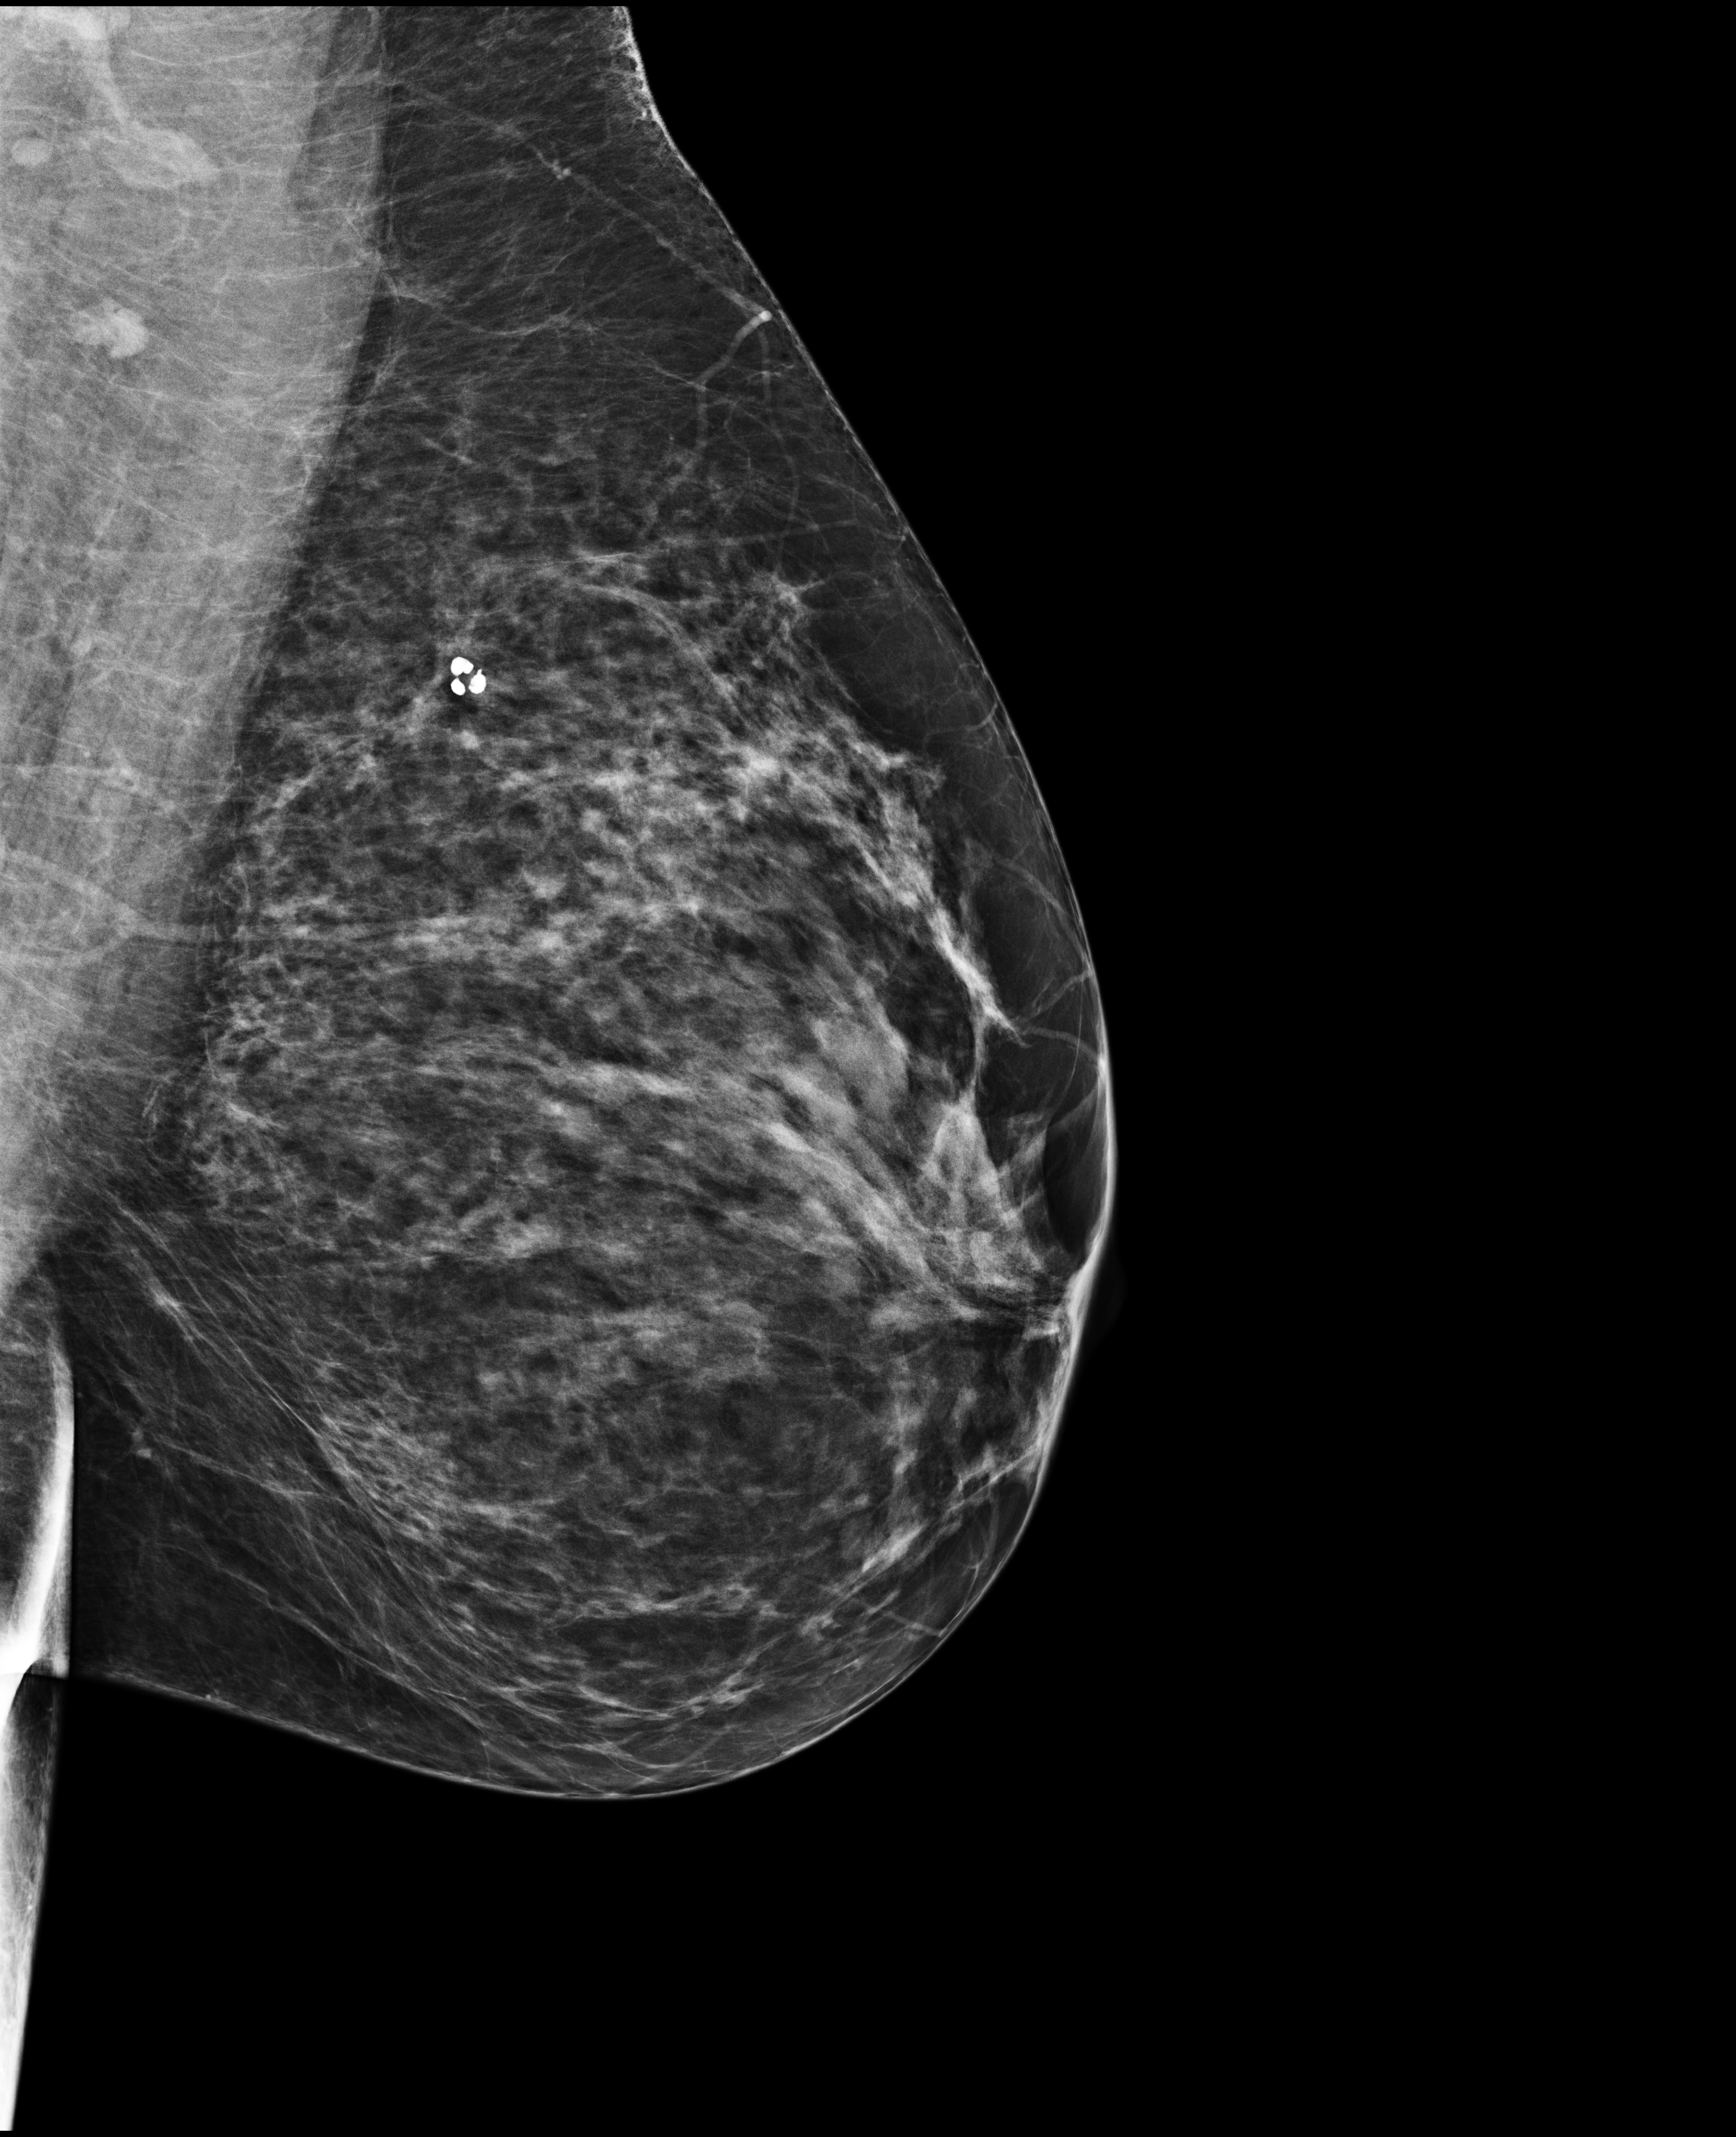
Full-field digital mammogram (FFDM); left breast; MLO view; screening examination; system: Selenia Dimensions. Female patient, age 61 years.
Breast density at the screening exam (both breasts): scattered fibroglandular densities (BI-RADS density category b). Final BI-RADS category for the screening round (tomosynthesis exam, both breasts): category 1. Recall: no recall after this screen.